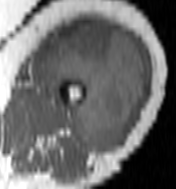
MRI of an extremity soft-tissue mass, one axial slice; slice 60 of 100 in the series (ordered by position); MR volume resampled by the dataset authors to the PET/CT grid (not the native acquisition matrix); 3.27 mm slice thickness; 176 × 189 image matrix, field of view 172 × 185 mm. Female patient. Case-level facts recorded for this patient, not image findings: histological type: undifferentiated – high grade; grade: high; site of the primary tumour: left thigh.
Outlined on this slice (expert contour drawn on MRI and transferred to this co-registered scan by the dataset authors):
- gross tumour volume including surrounding oedema: bounding box [x1, y1, x2, y2] px = [46, 23, 145, 149]
- gross tumour volume (mass): [46, 23, 143, 149]